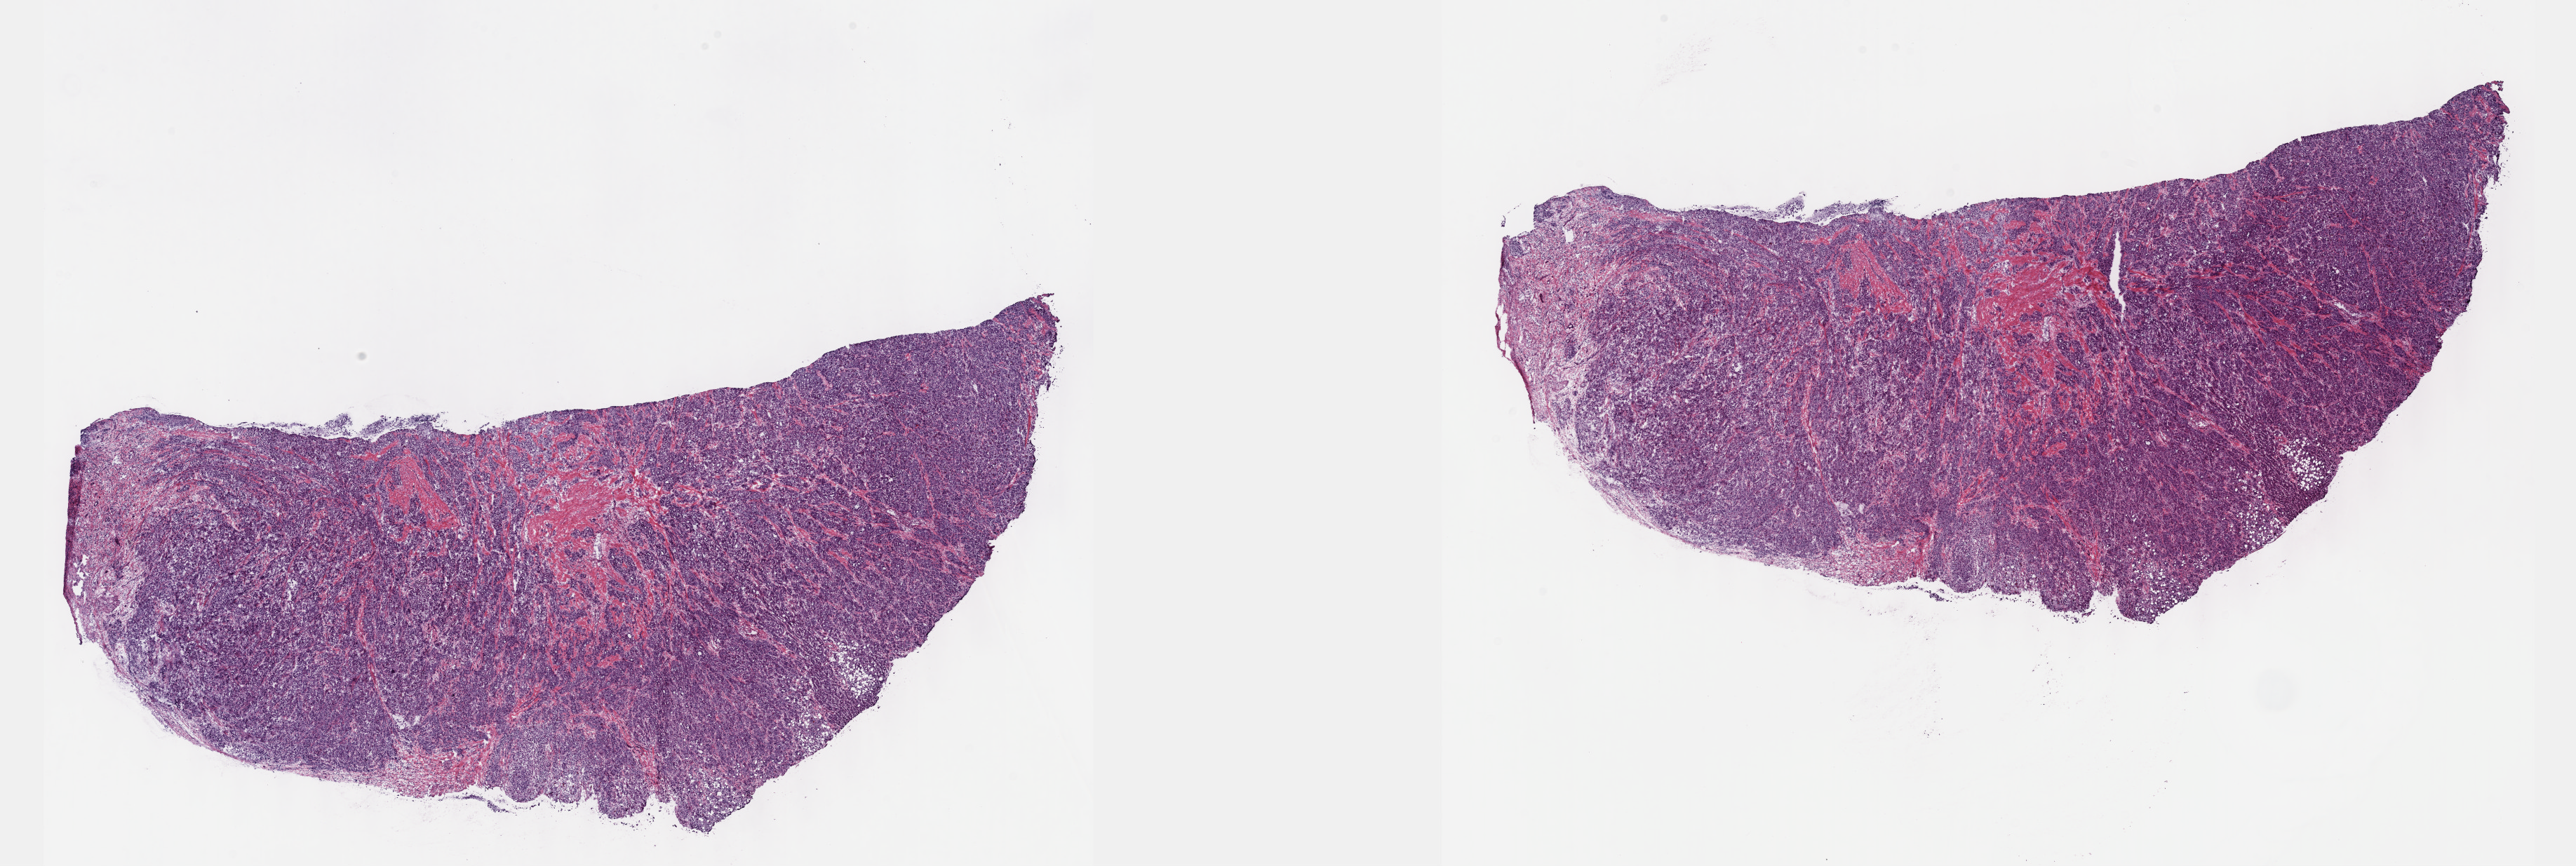
Hematoxylin and eosin (H&E) stained whole-slide image, whole scanned area (about 29.7 x 10.0 mm) shown as a low-resolution overview. Frozen section. Primary tumour sample from the liver. Male patient; age at initial diagnosis 62 years. Histologic grade: G2 (moderately differentiated). Slide review estimates, as recorded: tumour cells 100%, tumour nuclei 75%, normal cells 0%, stromal cells 0%, necrosis 0%. Inflammatory infiltration, as recorded: lymphocyte infiltration 2%, monocyte infiltration 0%, neutrophil infiltration 0%.
Diagnosis: Hepatocellular carcinoma, NOS. AJCC pathologic stage: II (7th edition).